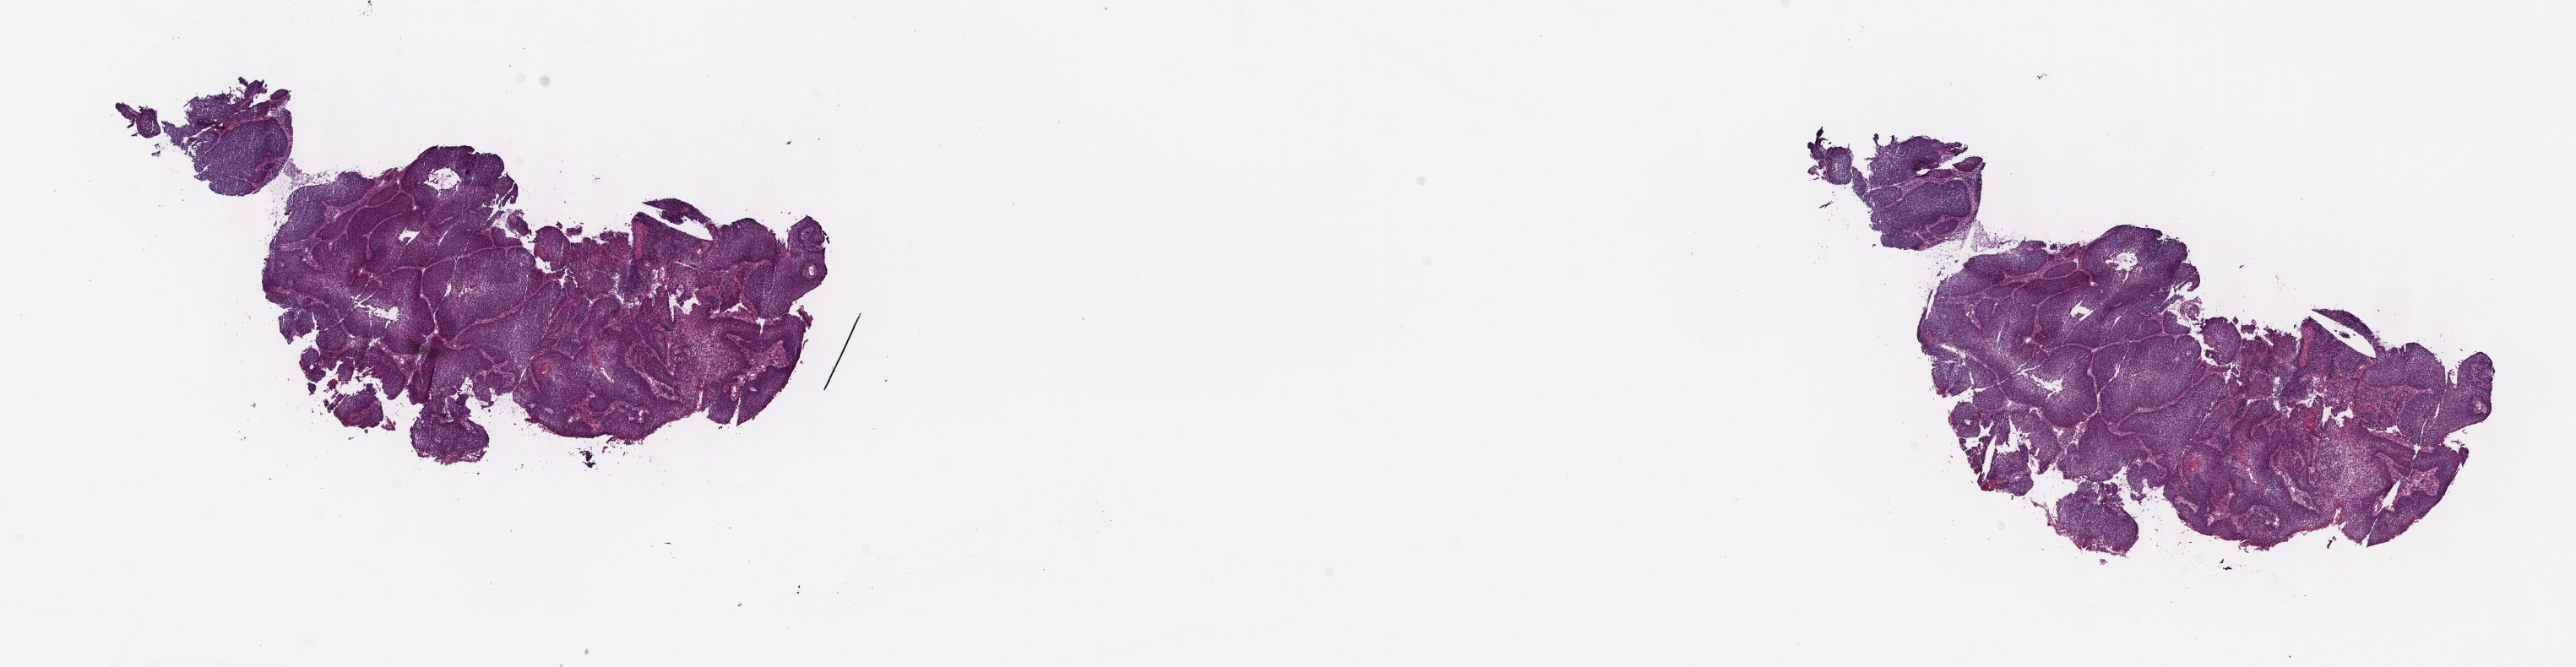
H&E-stained whole-slide image, shown as a low-resolution overview of the whole scanned area (about 24.7 x 6.4 mm). Frozen section from the top of the tissue portion. Primary tumour sample from the cervix. Female, age 42 years at initial diagnosis. Histologic grade: G2 (moderately differentiated). Pathologist review of this section (percent, as recorded): tumour cells 90%, tumour nuclei 90%, normal cells 5%, stromal cells 5%, necrosis 0%. Infiltration values recorded for this section: lymphocyte infiltration 3%, monocyte infiltration 0%, neutrophil infiltration 1%.
• histologic diagnosis: Squamous cell carcinoma, NOS
• FIGO stage: IIB